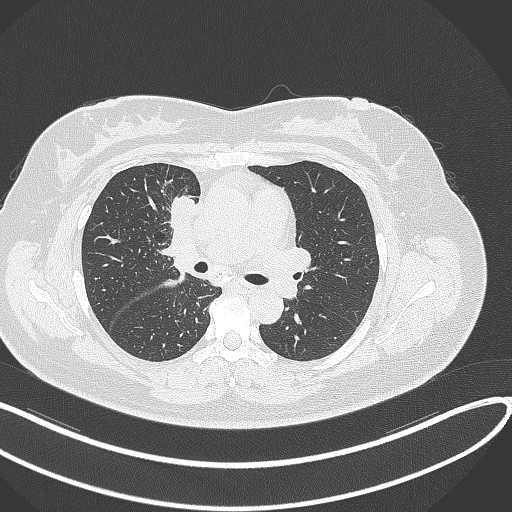
Chest CT, one axial slice. Slice 163 of 303 in the series (ordered by position). Reconstruction kernel B70f. Lung window (W 1500 / L -600 HU). 1 mm slice thickness. 512 × 512 image matrix. Patient: female, 46 years. From the clinical record (not read from this slice): clinical TNM (as recorded): T2a N1 M0.
Structures marked on this image (bounding box drawn by a radiologist):
- lung tumour (recorded histology: adenocarcinoma): box from (x=166, y=186) to (x=198, y=233) px